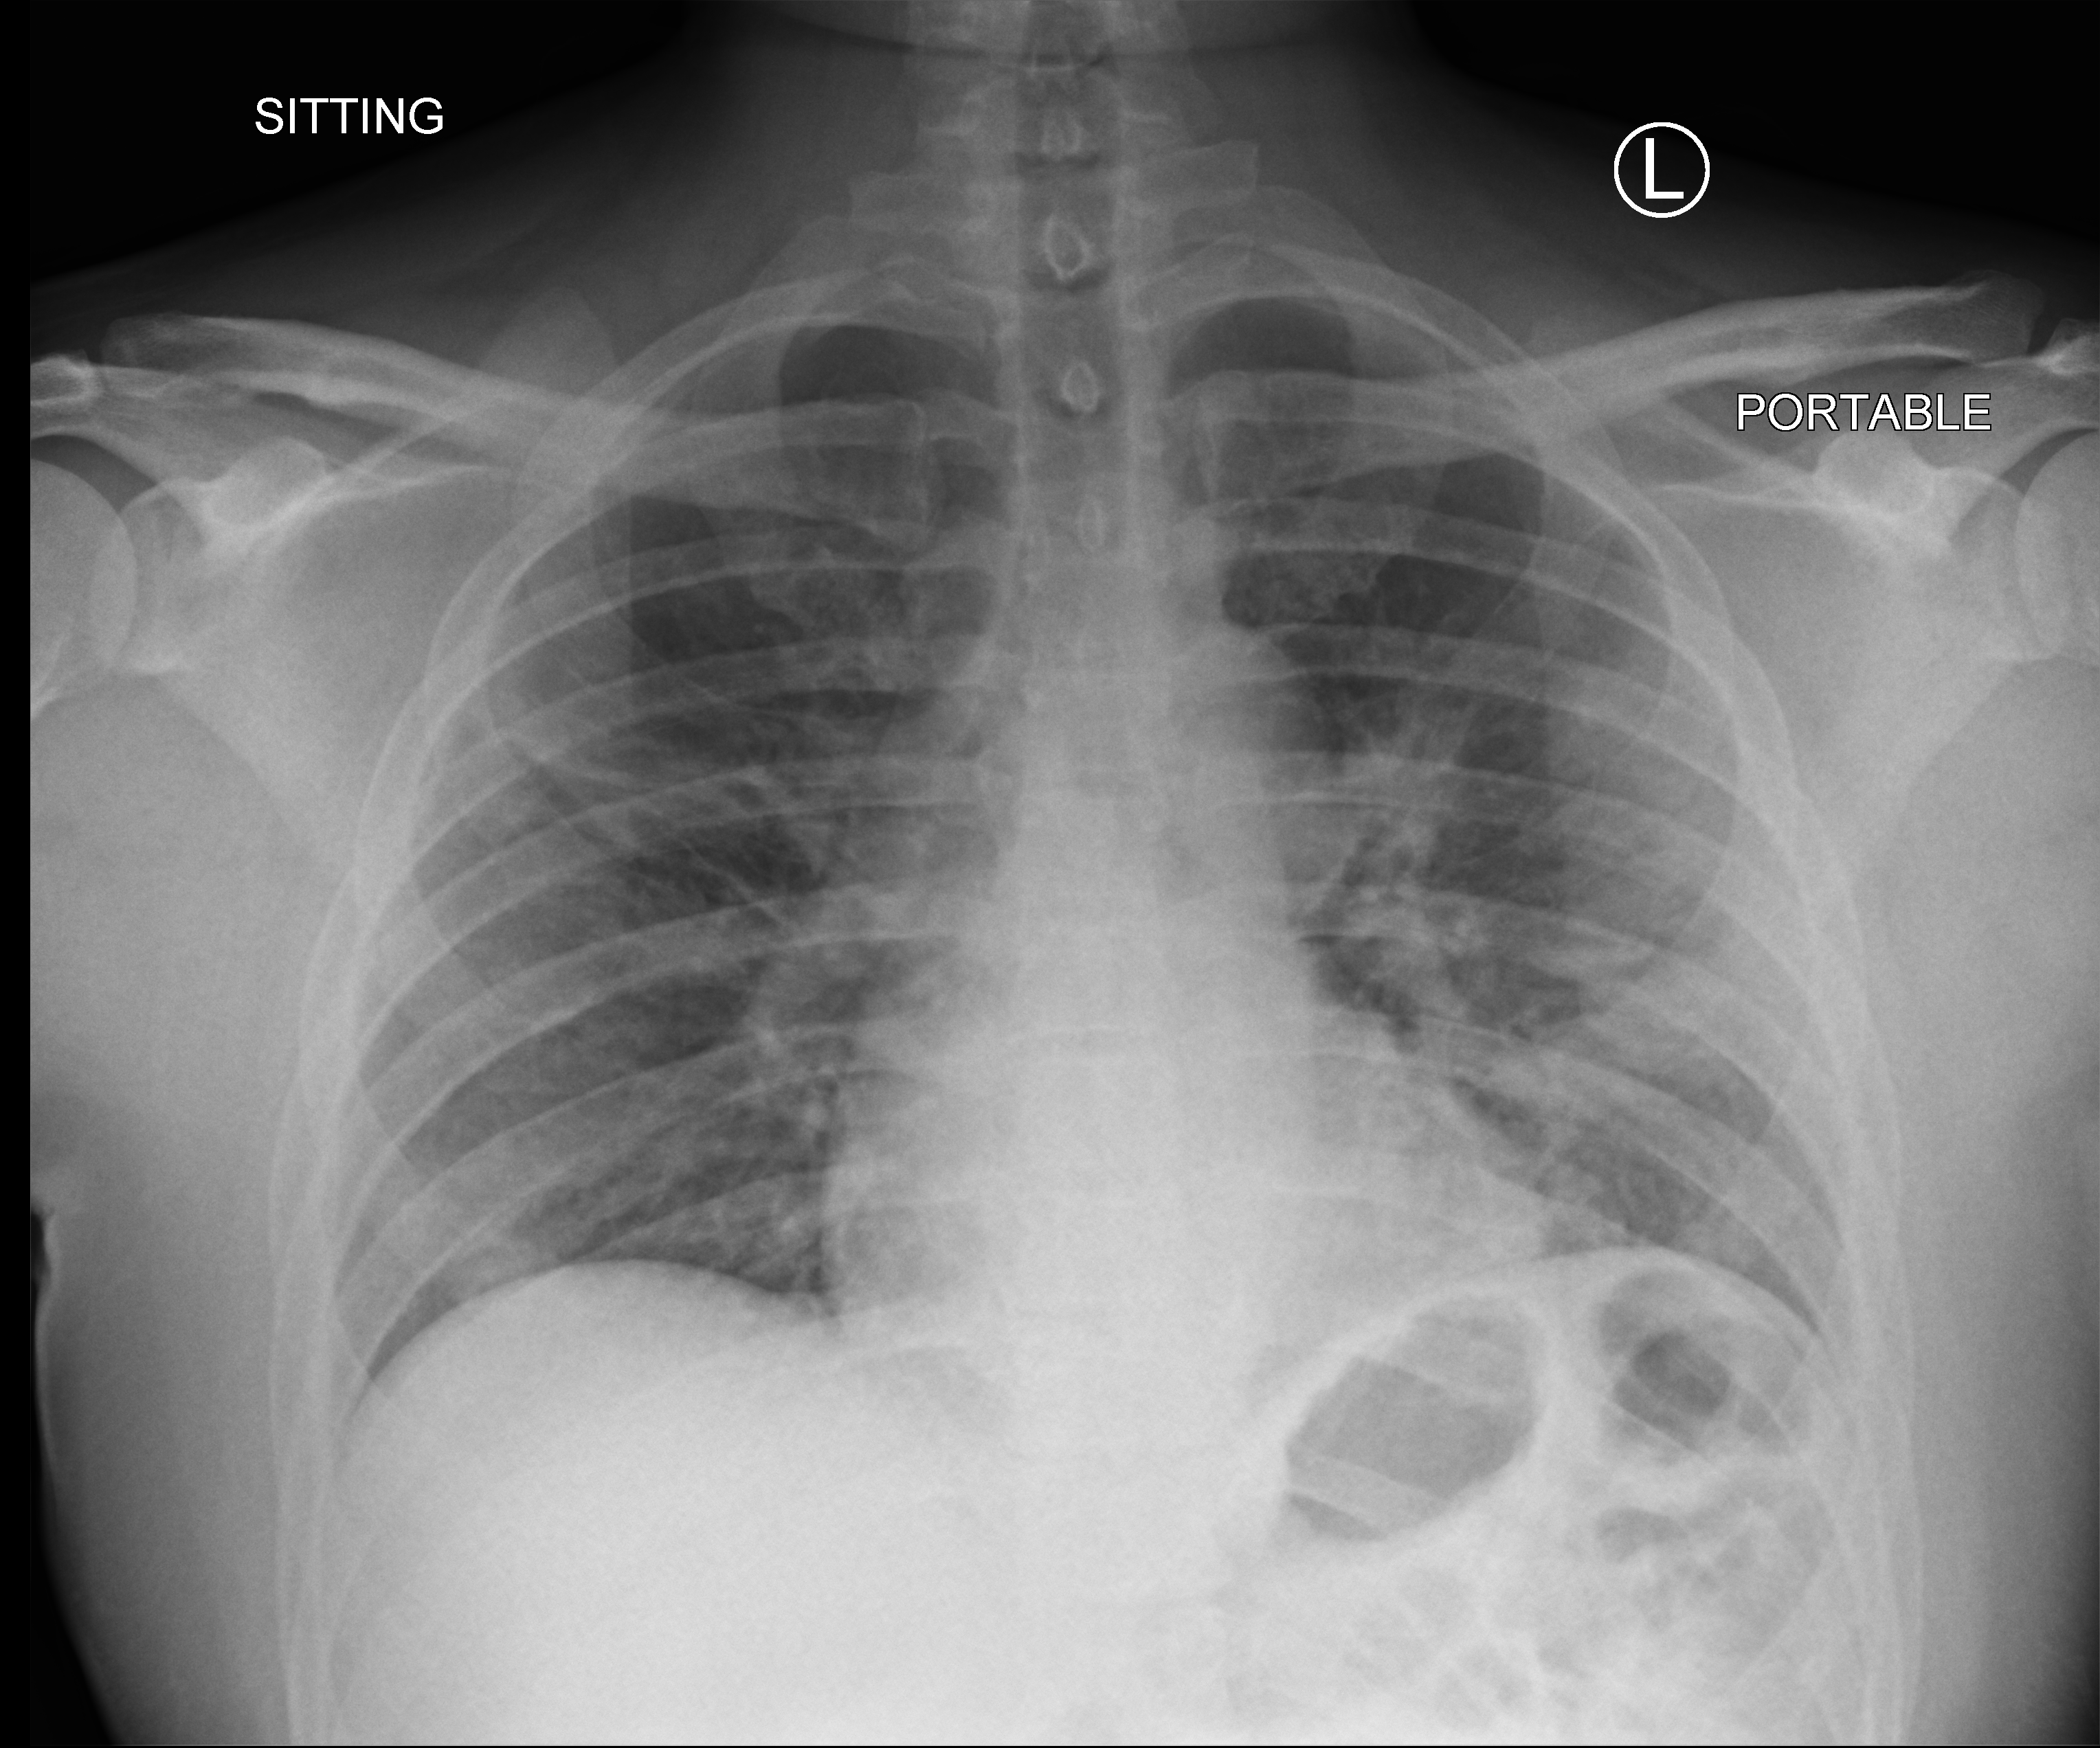
Chest X-ray (portable). Patient hospitalised with COVID-19; male, aged 18–59 years.
Admission-level facts for this patient (not findings on this image; timing relative to this image not recorded):
- admitted to intensive care during this hospital stay: no